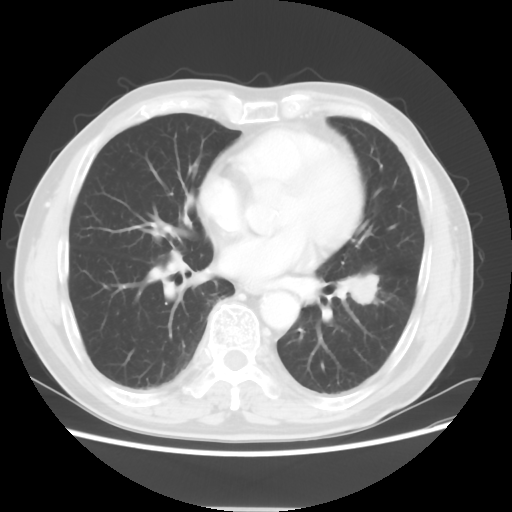
Chest CT, one axial slice; slice 25 of 64 in the series (ordered by position); 120 kVp; lung window (W 1500 / L -600 HU); 5 mm slice thickness; 512 × 512 image matrix, field of view 366 × 366 mm. Patient: male, 71 years. Case-level facts recorded for this patient, not image findings: clinical TNM (as recorded): T1c N1 M0; histopathological grade: G2-3.
Outlined on this slice (bounding box drawn by a radiologist):
- lung tumour (recorded histology: adenocarcinoma): bounding box <345,267,389,311> (left, top, right, bottom; pixels)